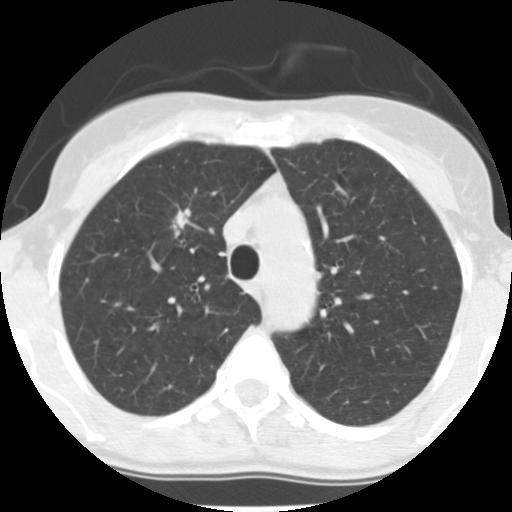
Axial slice from a low-dose chest CT screening exam, second screening round (one year after baseline), lung window (W 1500 / L -600 HU), 2.5 mm slice thickness, slice 42 of 150 in the series, 512 × 512 image matrix, field of view 280 × 280 mm. Female participant, aged 56 years at enrolment.
Expert-annotated lung lesion, bounding box (x1, y1, x2, y2) in pixels: (155, 204, 199, 246). The exam's reader record, not a measurement of the box and not confirmed to be the same lesion: non-calcified nodule or mass ≥4 mm, right upper lobe, 12 × 9 mm, spiculated (stellate) margins, soft tissue attenuation, pre-existing on the prior screen: yes; interval growth: no. Official screen result: positive, other. Lung cancer was diagnosed 350 days after this screen (after the third annual screen): adenocarcinoma, NOS, right upper lobe, moderately differentiated (G2), stage IA (AJCC 6th edition), 19 mm at pathology.